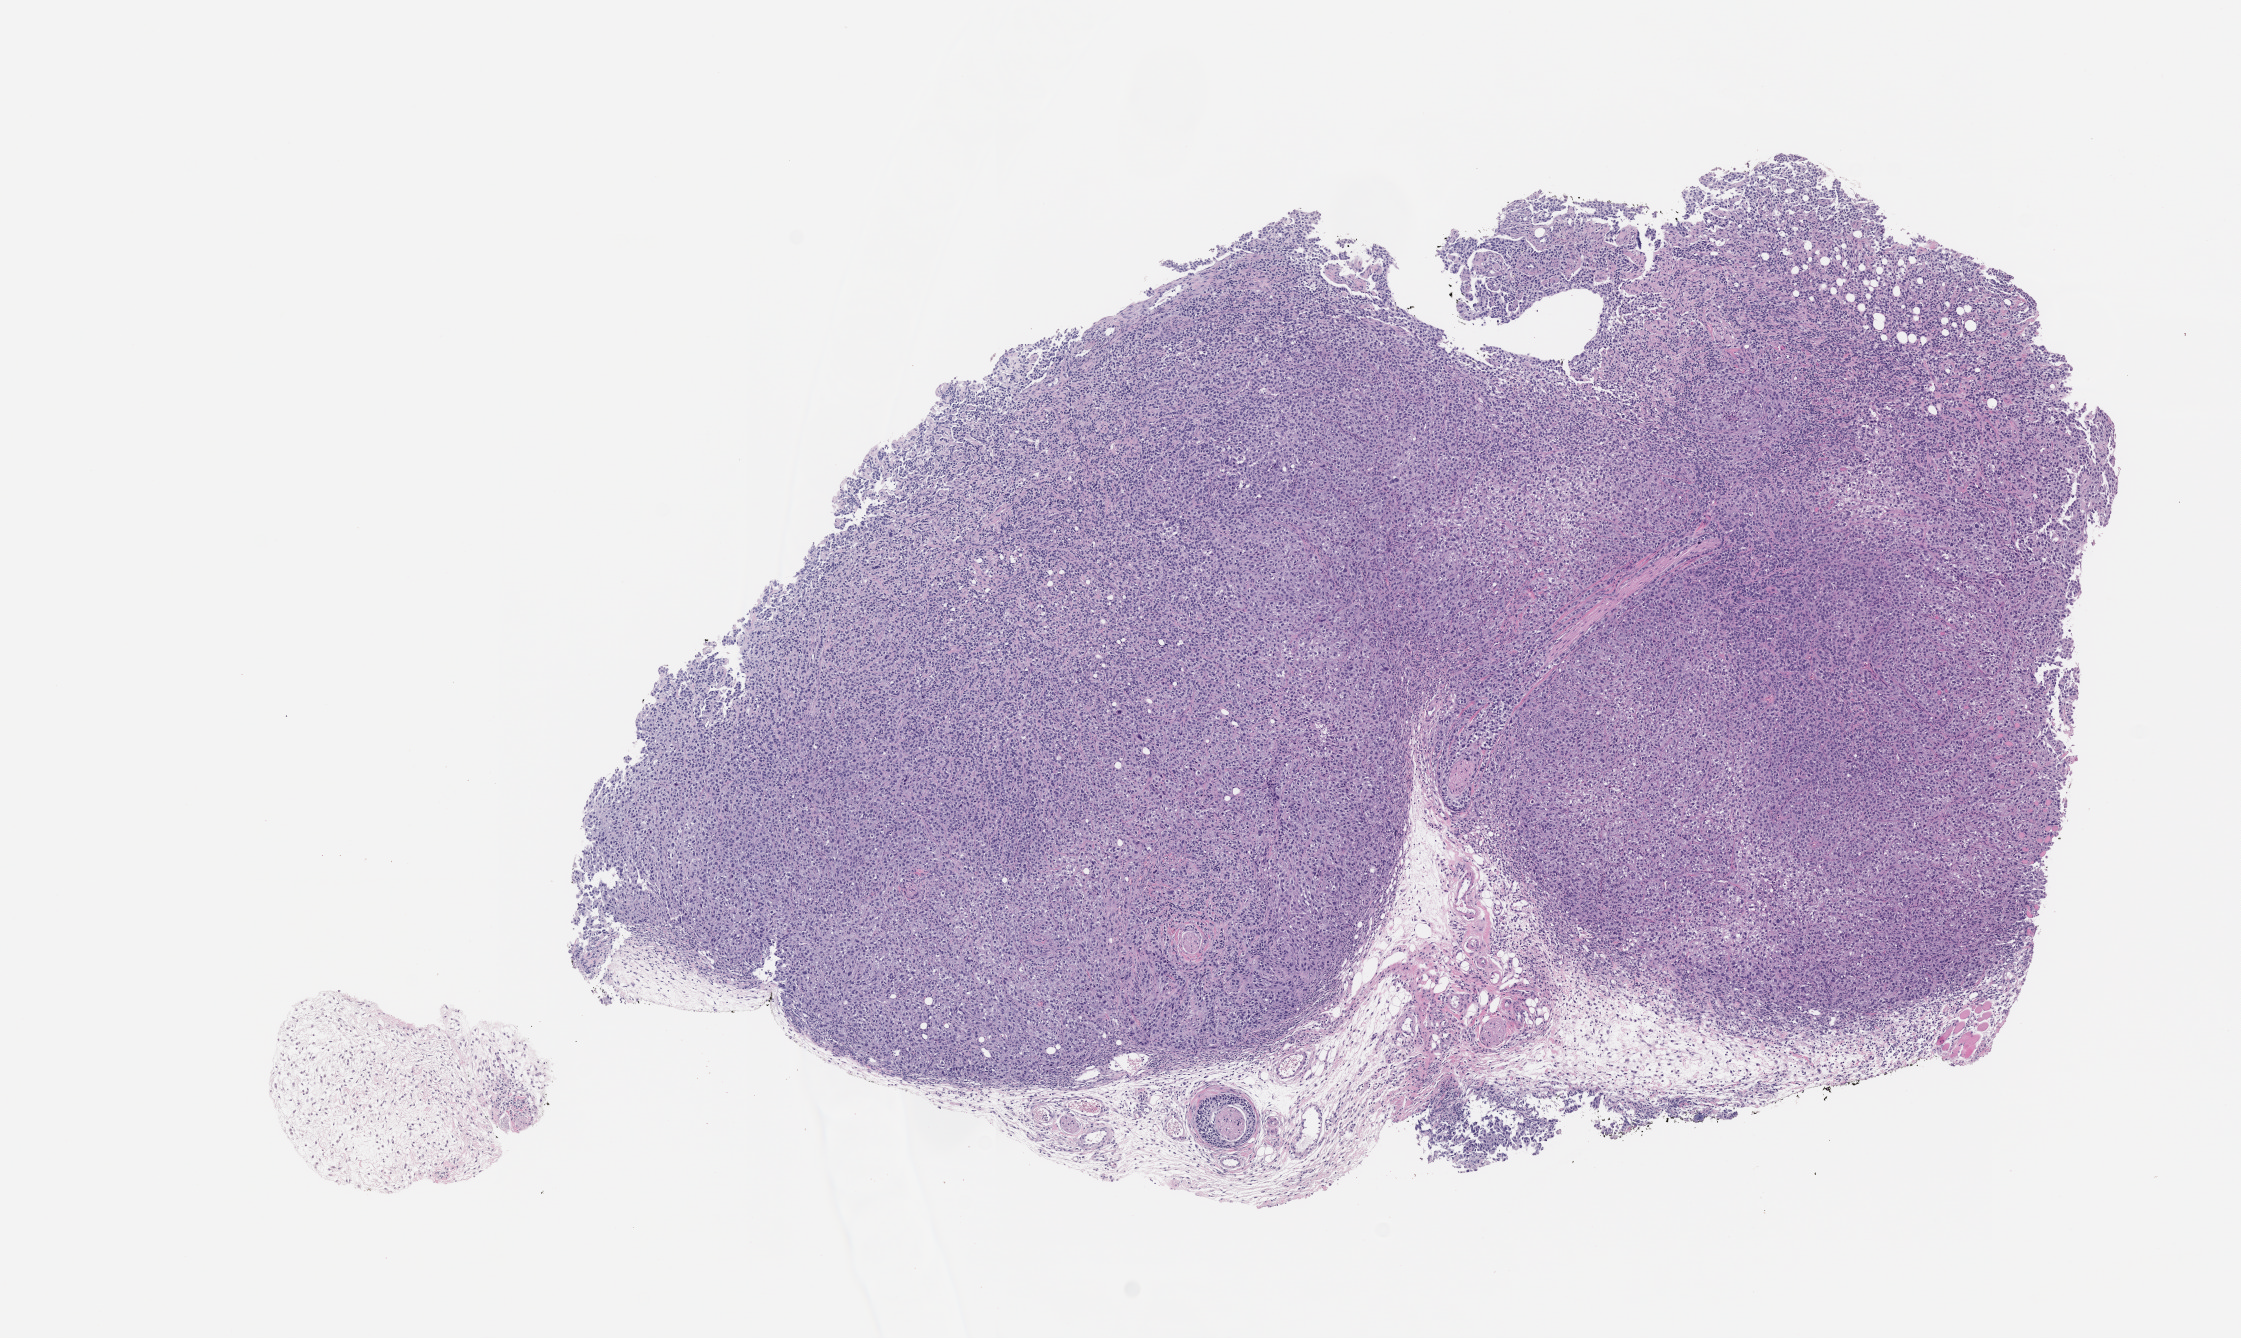
Whole-slide image, hematoxylin and eosin (H&E): patient-derived xenograft (human tumor grown in a mouse), passage 3, shown as a low-resolution overview of the whole scanned area (about 9.0 x 5.4 mm). Formalin-fixed, paraffin-embedded (FFPE) tissue. Originating tumor site category: bladder.
Originating patient diagnosis: Transitional Cell Carcinoma.